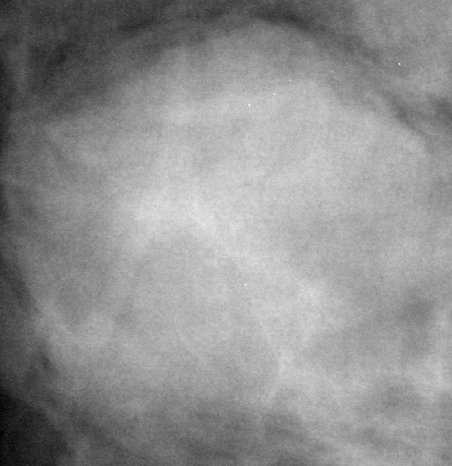
Crop from a digitized film mammogram around one marked abnormality; right breast; CC view.
- Finding: mass, shape oval, margins circumscribed; BI-RADS assessment category 4; subtlety rating 4 on a 1 (subtle) to 5 (obvious) scale; pathology result (as recorded, not read from the image): benign.